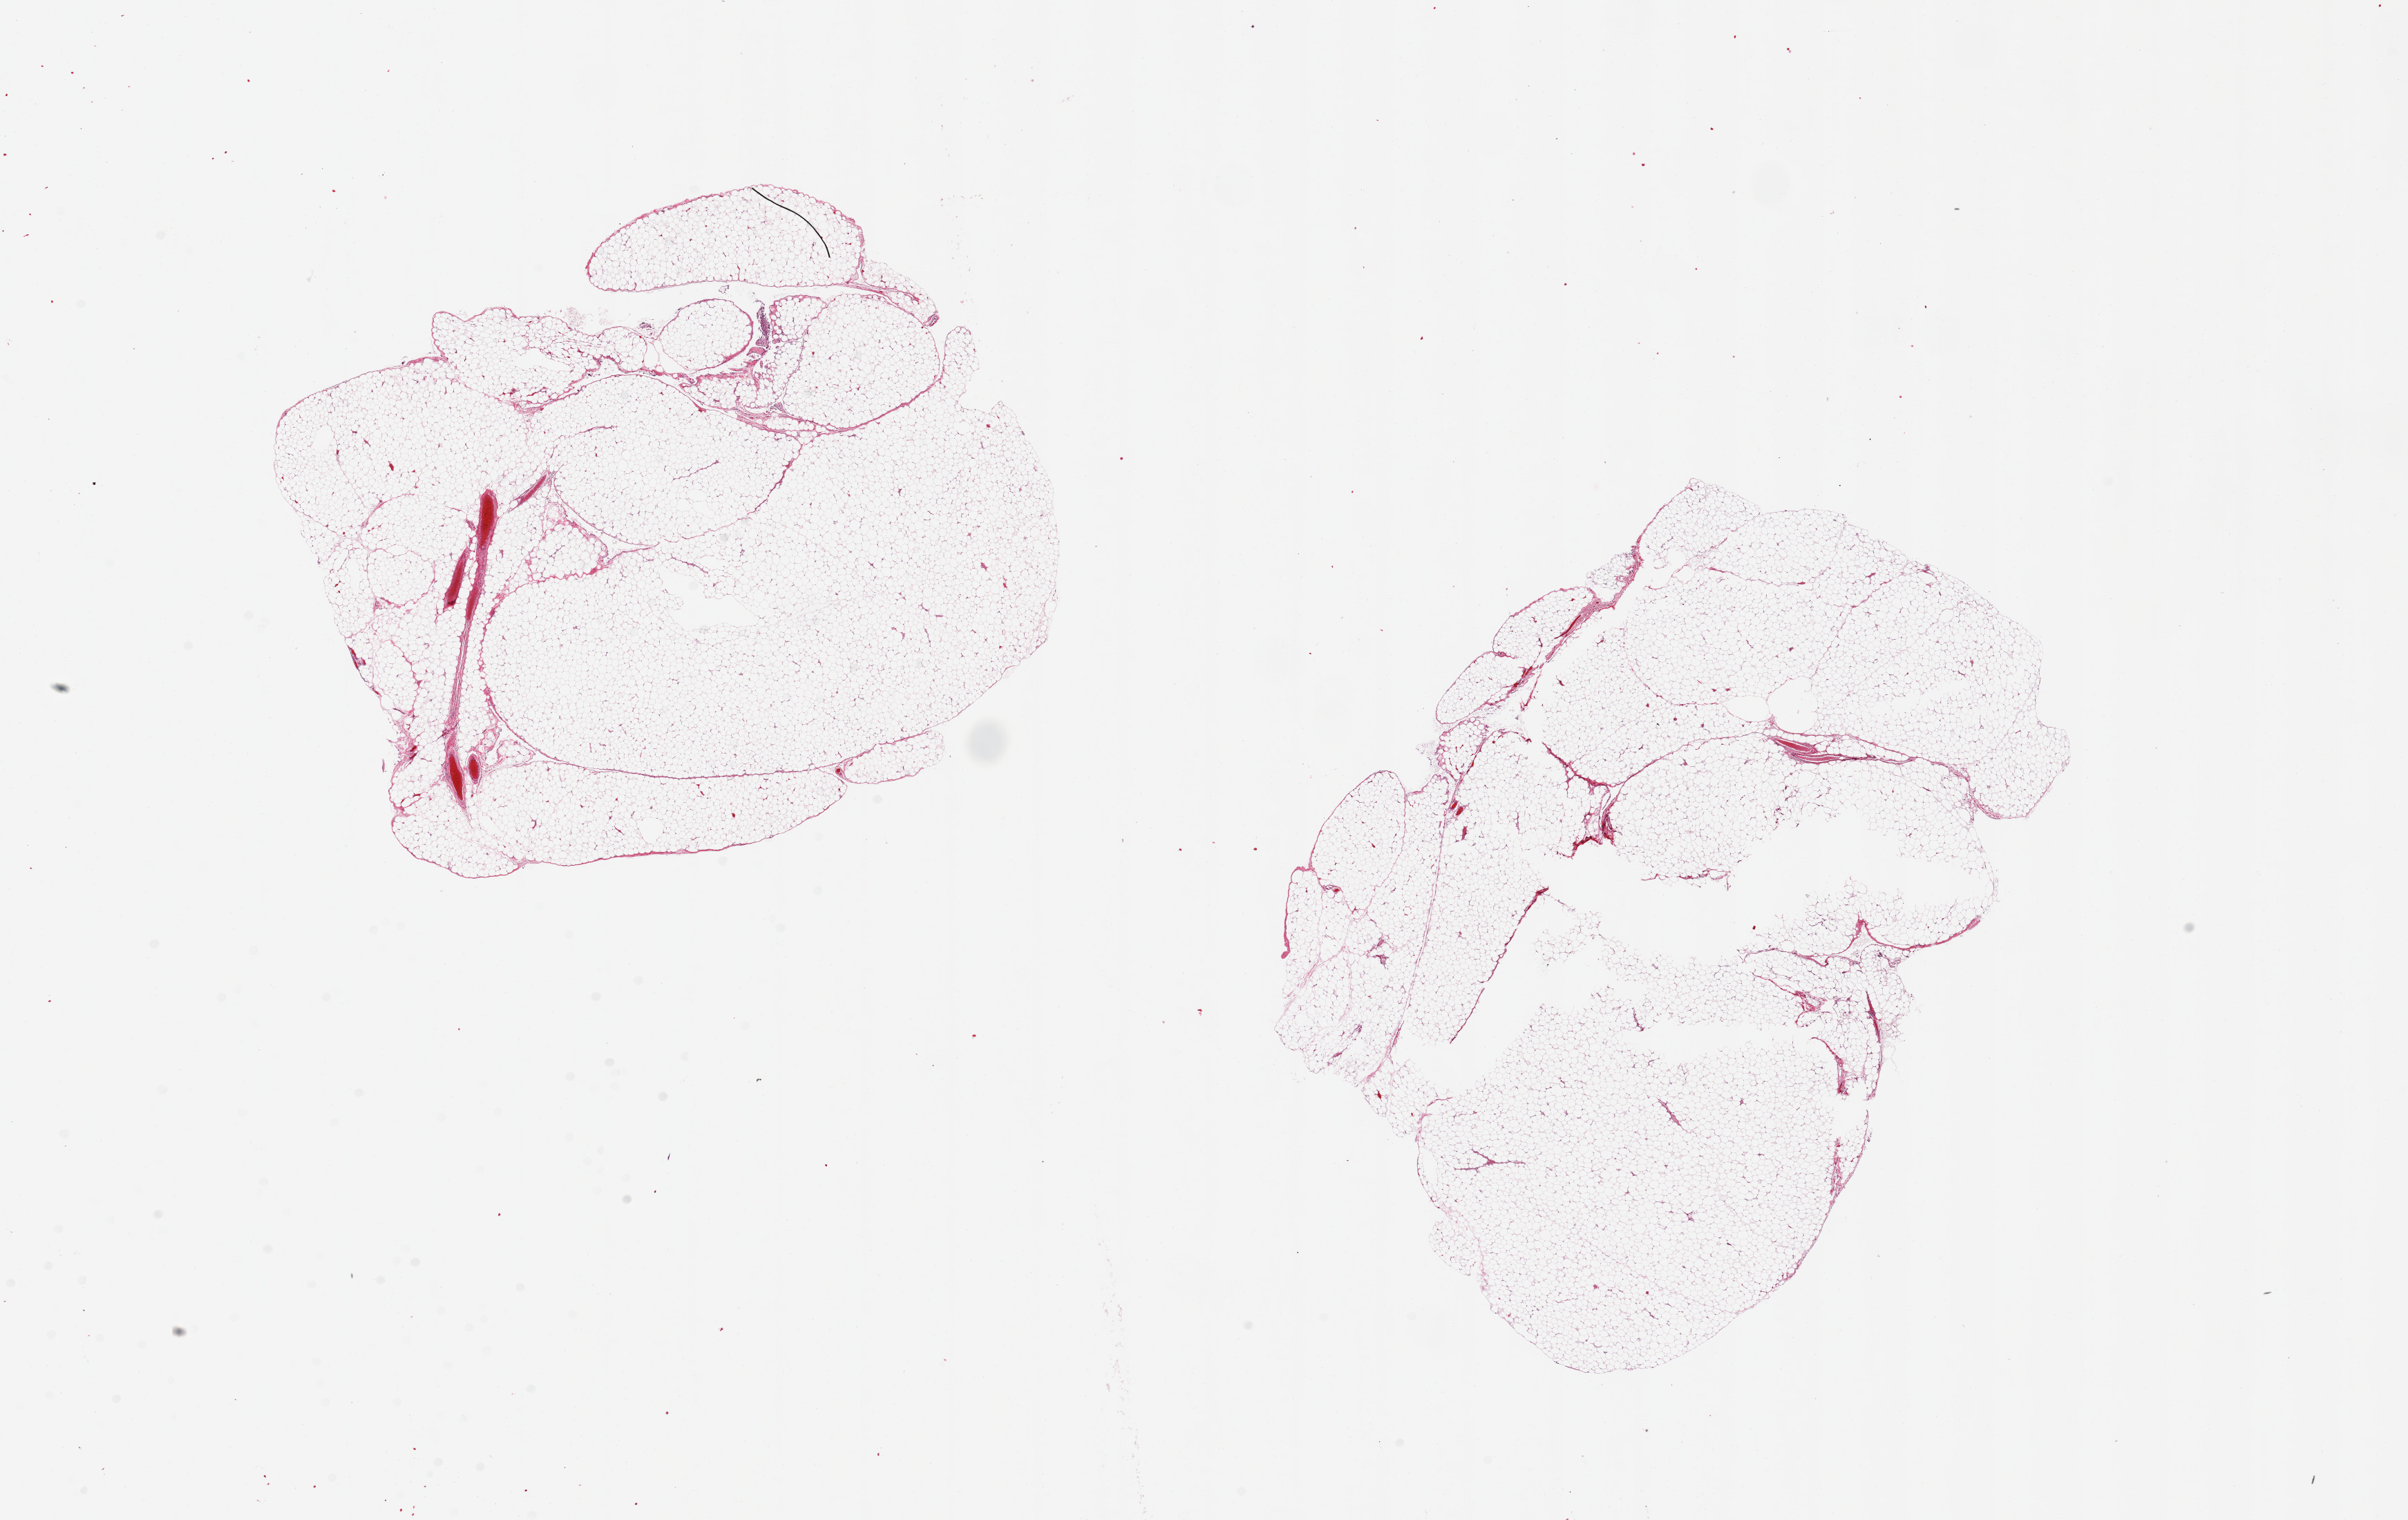
Whole-slide image, haematoxylin and eosin stain, a low-resolution overview of the entire scanned area, about 27.6 x 17.4 mm (from a 20x scan). PAXgene-fixed, paraffin-embedded tissue. Section of omentum (target tissue). Donor tissue sample. Donor sex: female.
• review note (as recorded): 2 pieces, 8x7 & 10x7mm; Central defects up to 3.8 x 1 mm